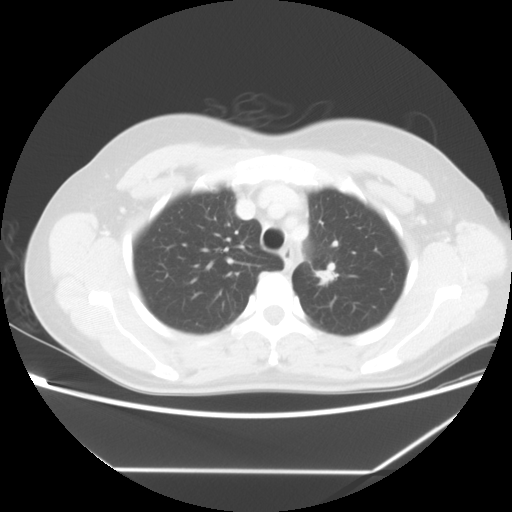
Chest CT, one axial slice; lung window (W 1500 / L -600 HU); 5 mm slice thickness; 512 × 512 image matrix. Female patient, age 43 years. Case-level facts recorded for this patient, not image findings: clinical TNM (as recorded): T1c N0 M1b.
Outlined on this slice (bounding box drawn by a radiologist):
- lung tumour (recorded histology: adenocarcinoma): bounding box (x1, y1, x2, y2) in pixels: (313, 265, 348, 298)